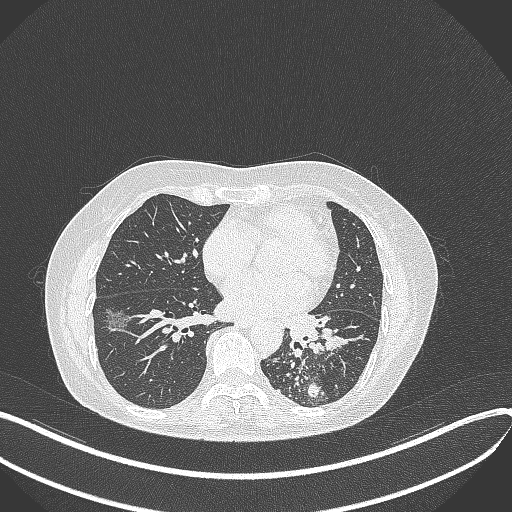
Chest CT, one axial slice; position 171 of 429 along the scan axis; 100 kVp; lung window (W 1500 / L -600 HU); 512 × 512 image matrix. Female patient, age 63 years. Case-level facts recorded for this patient, not image findings: clinical TNM (as recorded): T1b N0 M0.
Structures marked on this image (rectangle marked by the reading radiologist):
- lung tumour (recorded histology: adenocarcinoma): bounding box (x1, y1, x2, y2) in pixels: (279, 305, 349, 356)